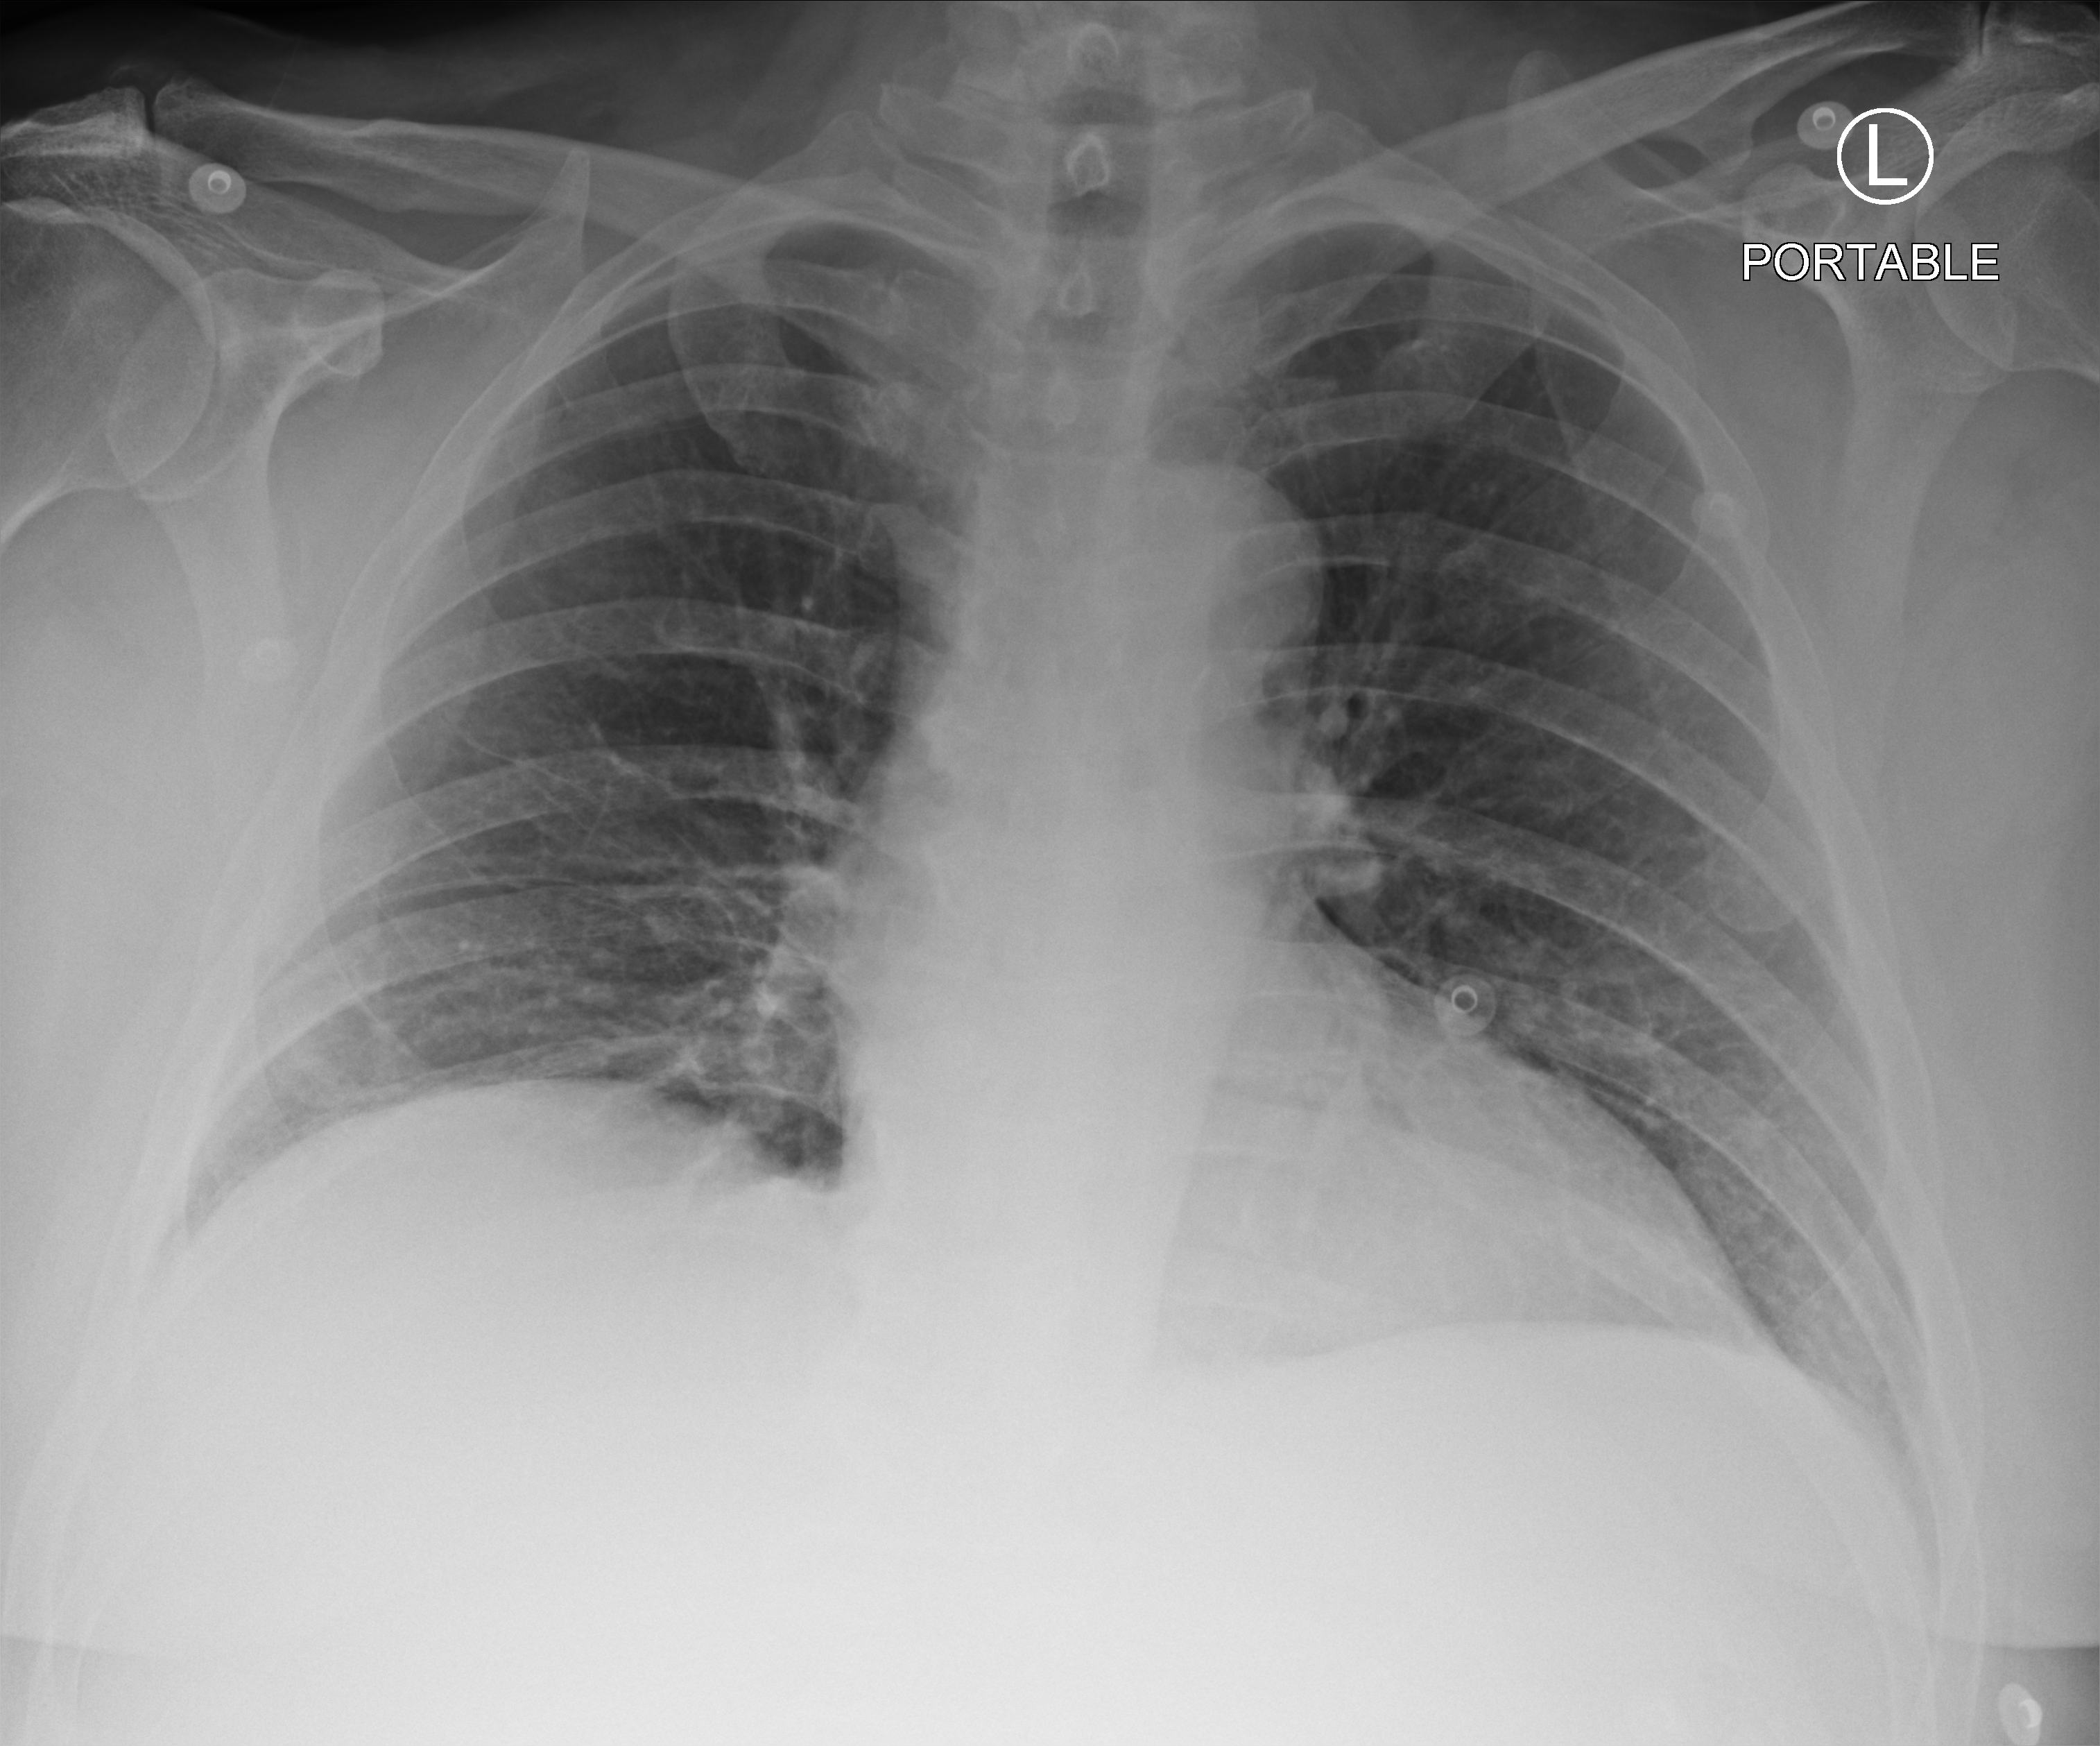
Portable chest radiograph; anteroposterior (AP) projection. Patient hospitalised with COVID-19; male, aged 60–74 years.
Admission-level facts for this patient (not findings on this image; timing relative to this image not recorded):
- mechanically ventilated during this hospital stay: no
- admitted to intensive care during this hospital stay: no